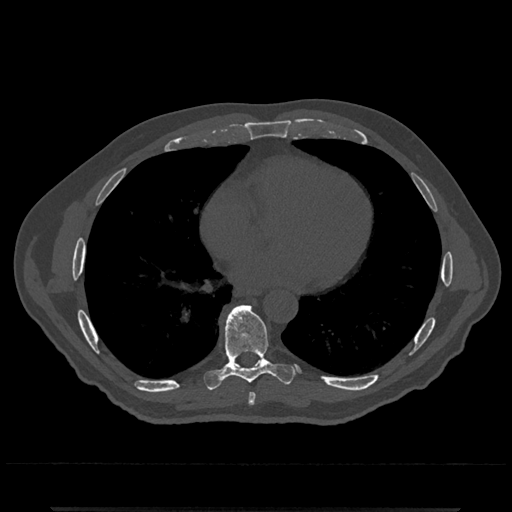
CT including the spine, one axial slice. Position 669 of 797 along the scan axis. Reconstruction kernel Br40s/3. Bone window (W 1800 / L 400 HU). 0.5 mm slice thickness. 512 × 512 image matrix, field of view 393 × 393 mm. Male patient, age 67 years. From the clinical record (not read from this slice): primary cancer: prostate.
Outlined on this slice (semi-automatically segmented with operator editing):
- T7 vertebra: bounding box (x1, y1, x2, y2) in pixels: (248, 392, 256, 405)
- T8 vertebra: (204, 305, 295, 390)